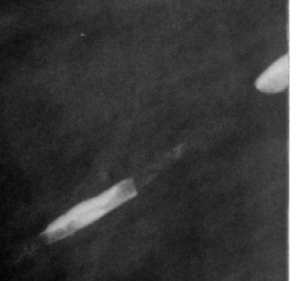
Cropped region of a digitized screen-film mammogram centred on a radiologist-marked abnormality; right breast; MLO view; BI-RADS breast density category 4 (scale 1–4).
Calcifications, morphology vascular; BI-RADS assessment category 2; subtlety rating 5 on a 1 (subtle) to 5 (obvious) scale; benign; no additional work-up was recommended (benign without callback).